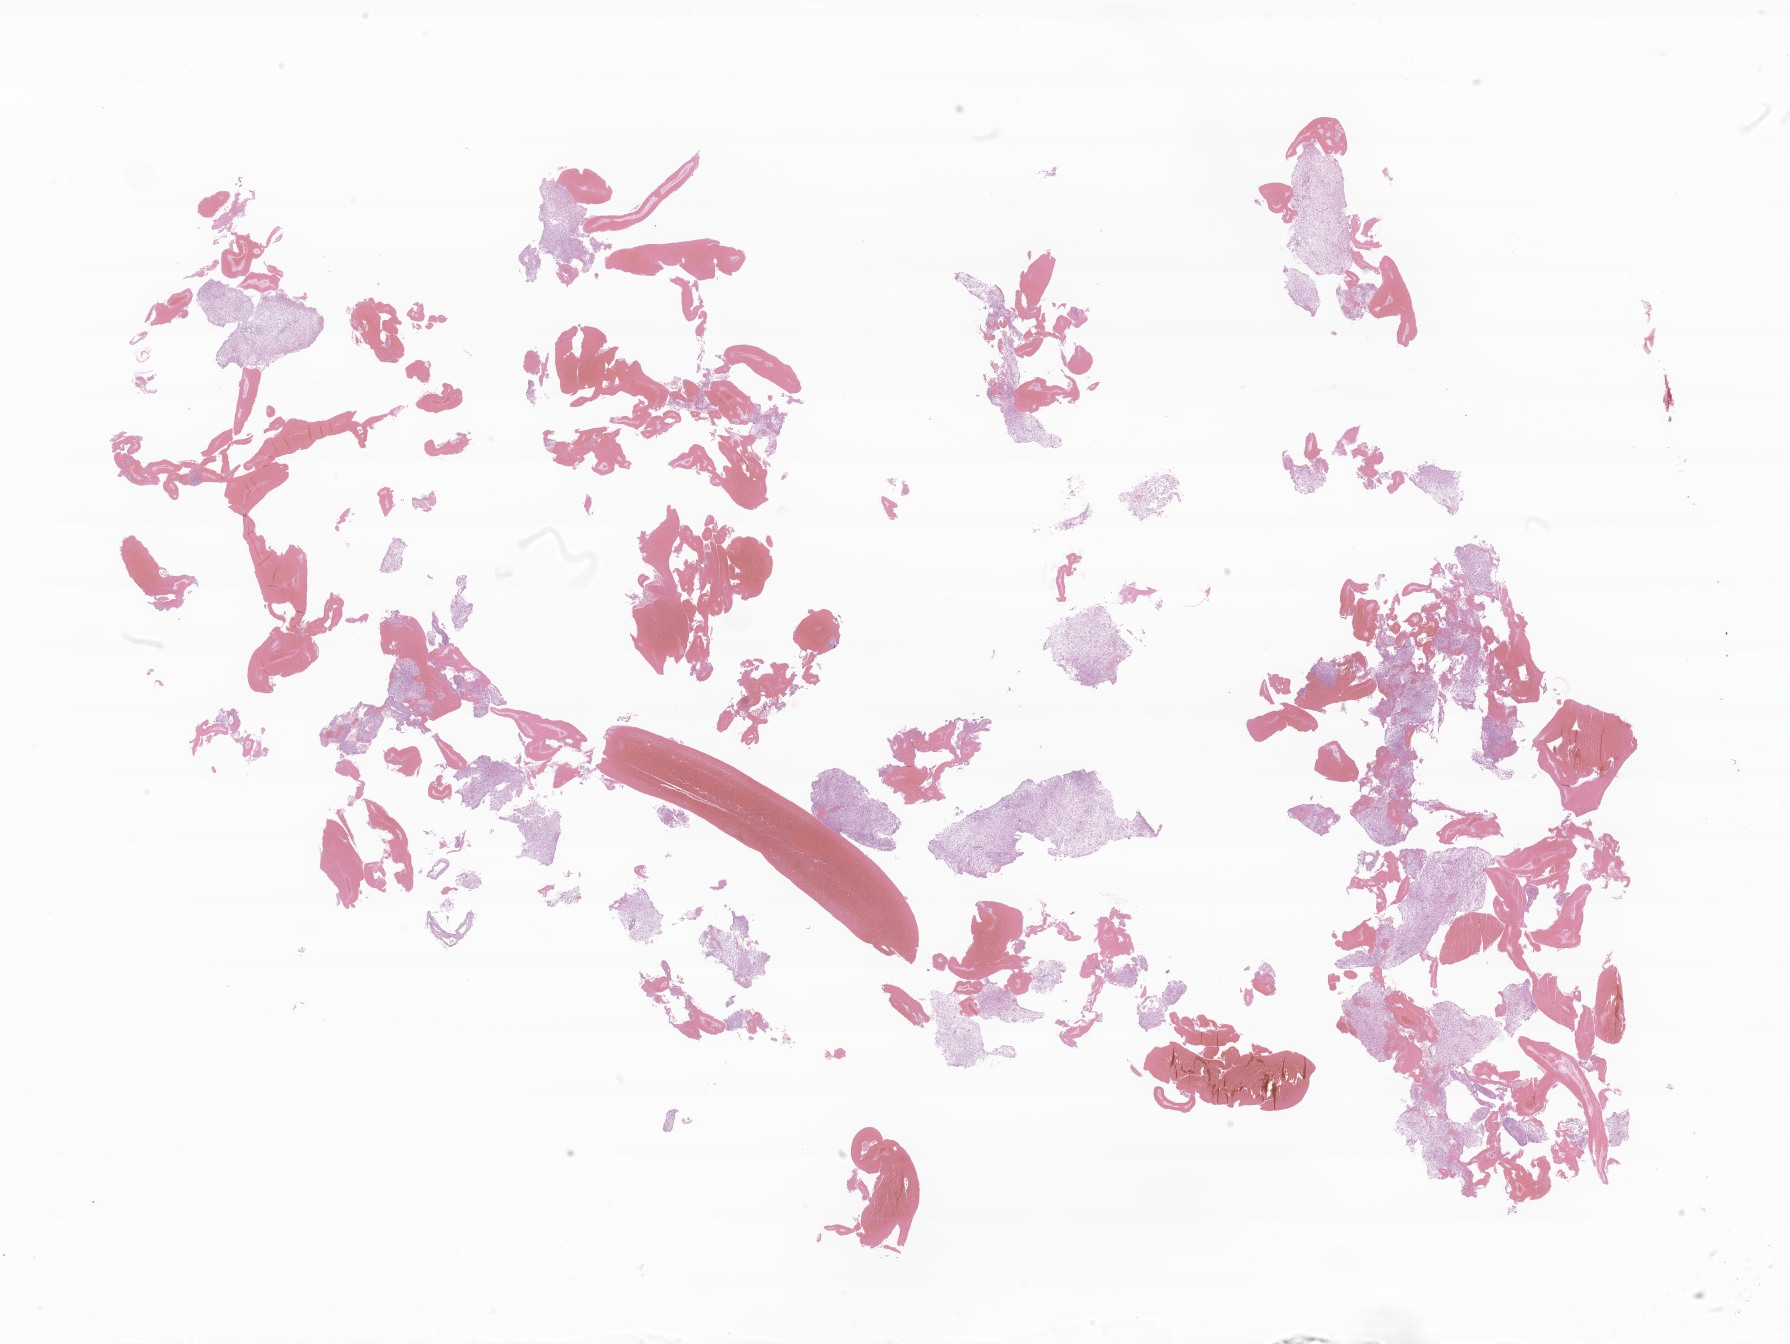
Whole-slide image, H&E stain of tumor tissue from the brain — a low-resolution overview of the entire scanned area, about 30.2 x 22.7 mm, FFPE section. Patient female; age 204 months (17 years).
Diagnosis: Astrocytoma, NOS.